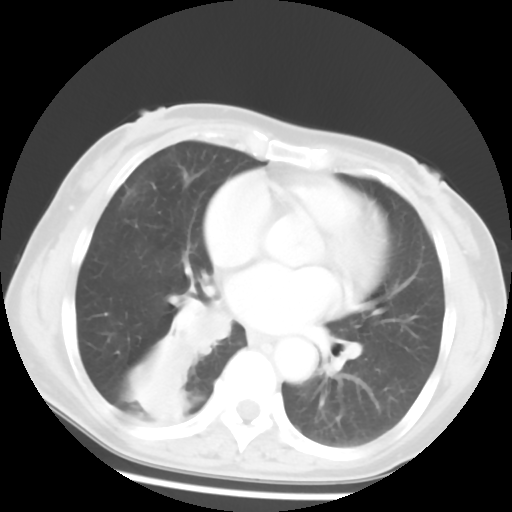
Chest CT, one axial slice; reconstruction kernel STANDARD; 120 kVp; lung window (W 1500 / L -600 HU); 5 mm slice thickness; 512 × 512 image matrix, field of view 297 × 297 mm. Female patient, age 54 years. From the clinical record (not read from this slice): clinical TNM (as recorded): T1c N0 M0.
Annotated regions visible in this slice (rectangle marked by the reading radiologist):
- lung tumour (recorded histology: squamous cell carcinoma): bounding box (x1, y1, x2, y2) in pixels: (171, 287, 236, 358)